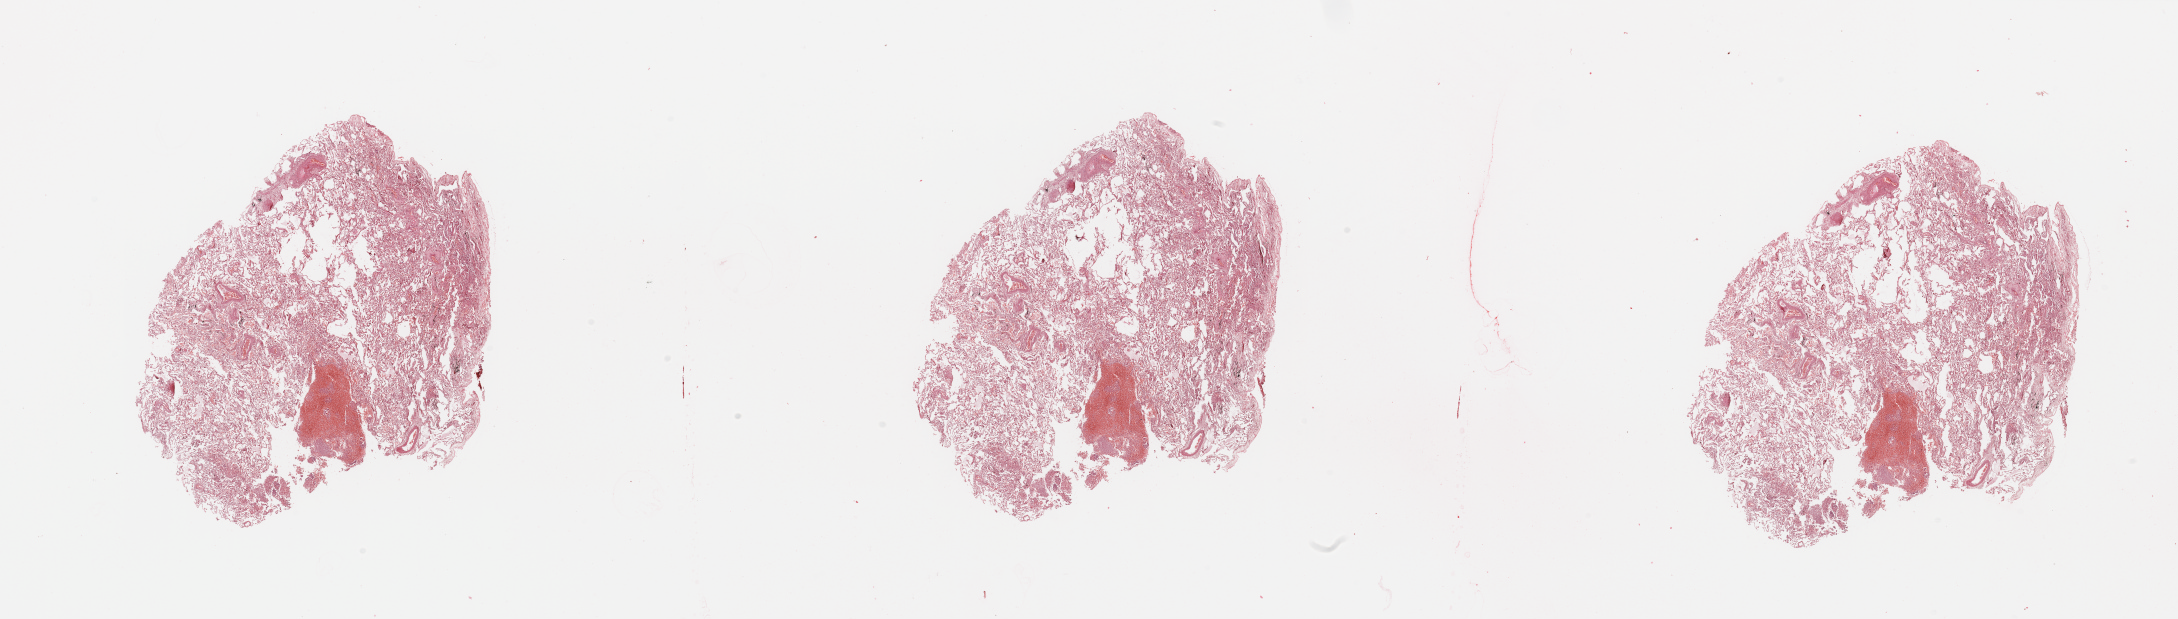
Whole-slide histology image, Hematoxylin and eosin (H&E) stained — shown as a low-resolution overview of the whole scanned area (about 34.5 x 9.8 mm, slide scanned at 20x), normal (non-tumour) tissue sample, lung. Patient: male, age 71 years.
This section: normal (non-tumour) tissue from the same patient. Patient diagnosis (cohort enrolment): squamous cell carcinoma (lung).